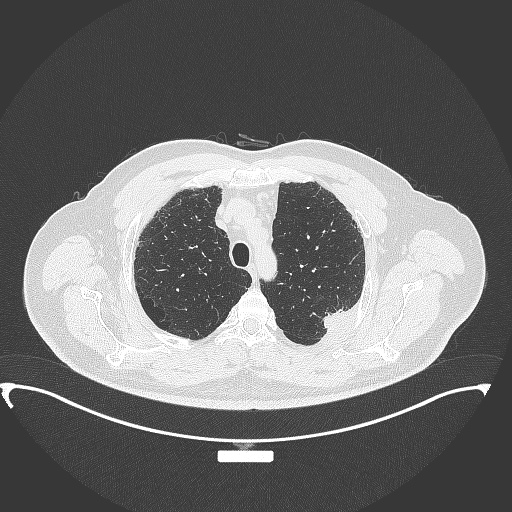
Chest CT, one axial slice. Slice 289 of 350 in the series (ordered by position). Reconstruction kernel B70f. 120 kVp. Lung window (W 1500 / L -600 HU). 1 mm slice thickness. 512 × 512 image matrix, field of view 459 × 459 mm. Male patient, age 64 years. From the clinical record (not read from this slice): clinical TNM (as recorded): T1c N1 M1.
Annotated regions visible in this slice (bounding box drawn by a radiologist):
- lung tumour (recorded histology: adenocarcinoma): bounding box (x1, y1, x2, y2) in pixels: (316, 301, 352, 335)